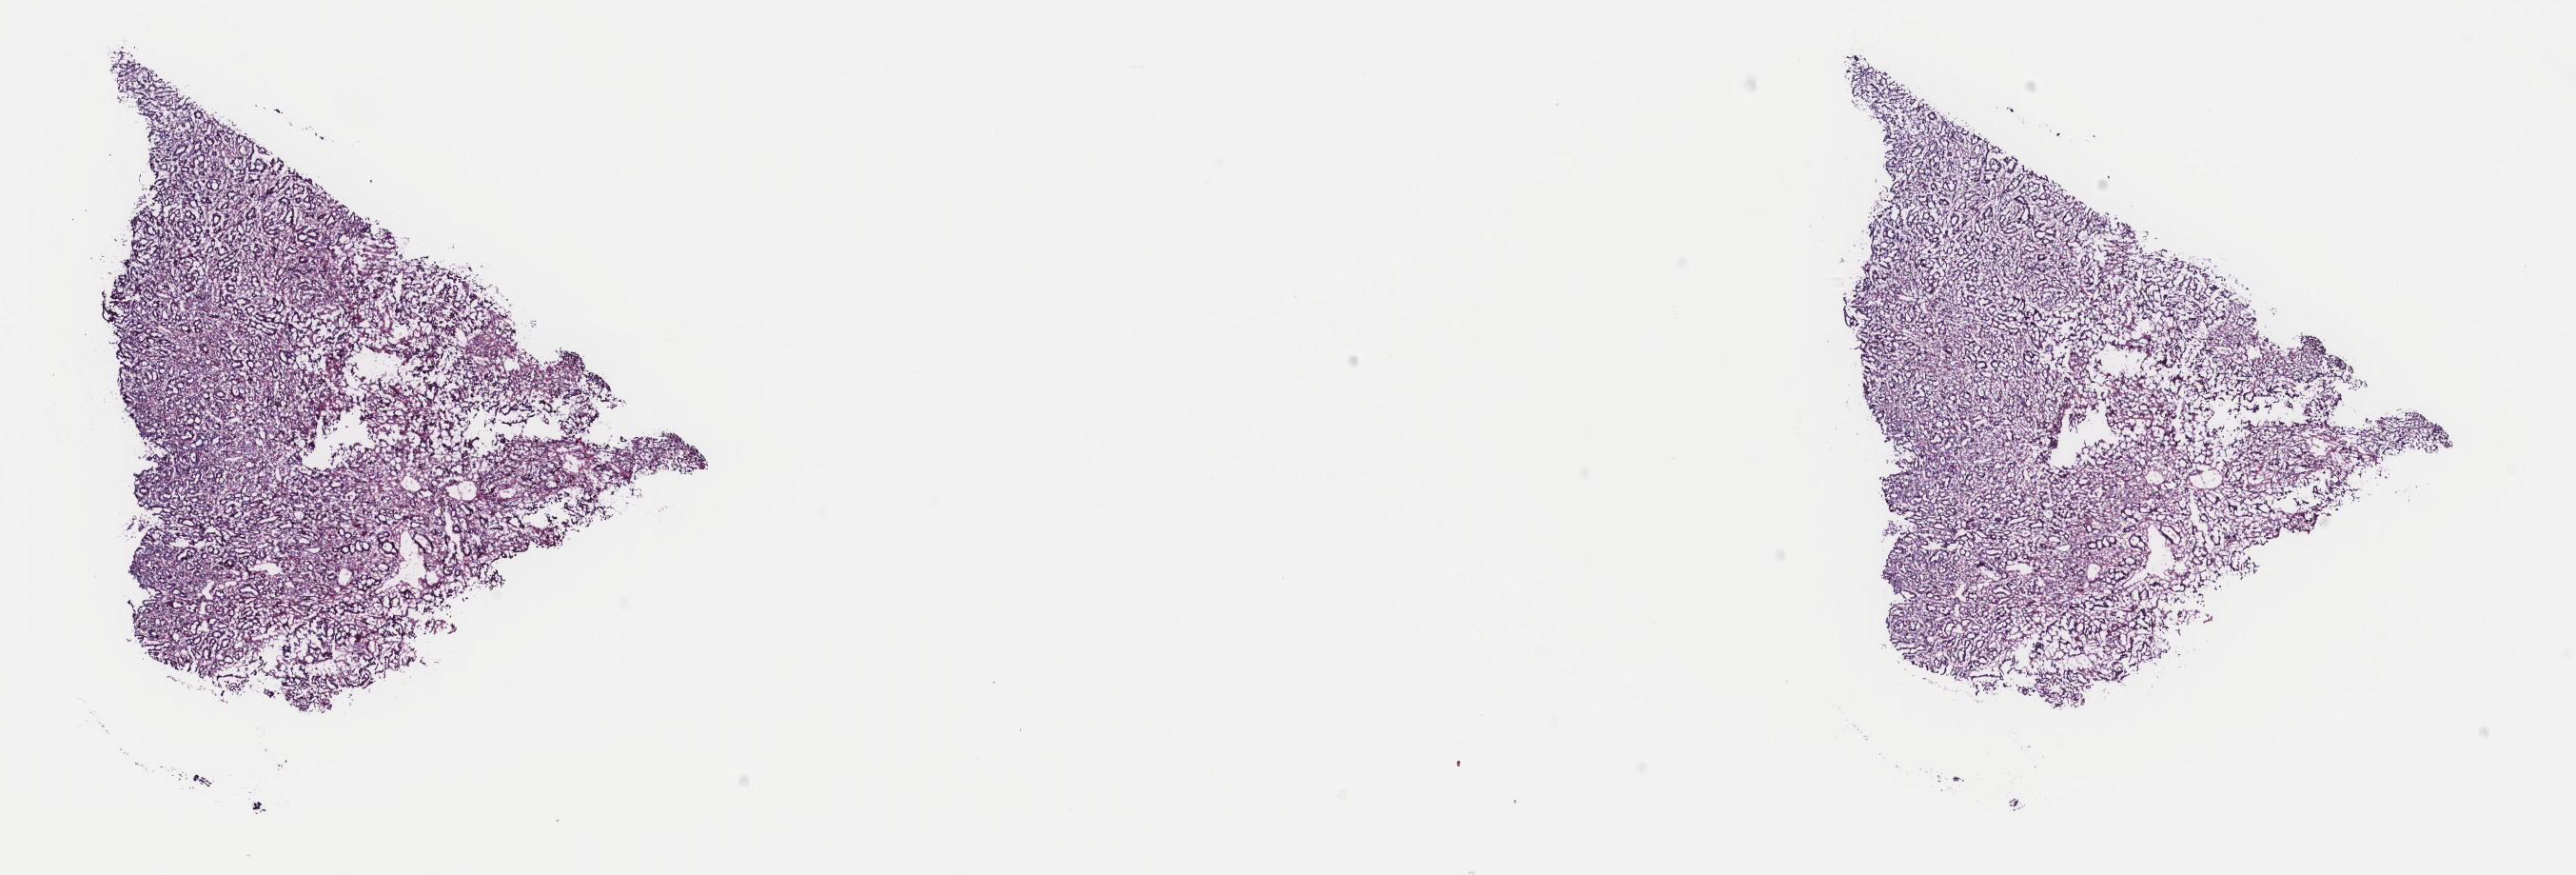
Hematoxylin and eosin (H&E) stained whole-slide image — shown as a low-resolution overview of the whole scanned area (about 21.5 x 7.3 mm), frozen section, sample: primary tumour, stomach. Male, age 63 years at initial diagnosis. Histologic grade: G3 (poorly differentiated). Composition of this section per pathologist review: tumour cells 75%, tumour nuclei 75%, normal cells 0%, stromal cells 24%, necrosis 1%. Infiltration values recorded for this section: lymphocyte infiltration 4%, monocyte infiltration 2%, neutrophil infiltration 5%.
Lymph nodes positive (case pathology): 7 of 28 examined. Histologic diagnosis: Adenocarcinoma, NOS (cardia, NOS).